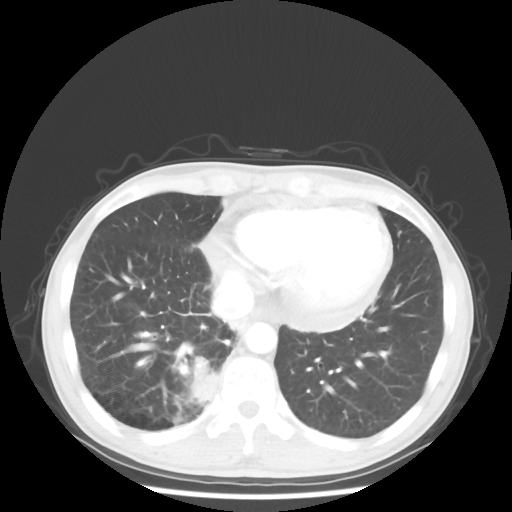
Chest CT, one axial slice. Position 14 of 58 along the scan axis. 100 kVp. Lung window (W 1500 / L -600 HU). 512 × 512 image matrix. Patient: male, 56 years. From the clinical record (not read from this slice): clinical TNM (as recorded): T2 N1 M1.
Structures marked on this image (rectangle marked by the reading radiologist):
- lung tumour (recorded histology: adenocarcinoma): box from (x=181, y=356) to (x=221, y=403) px